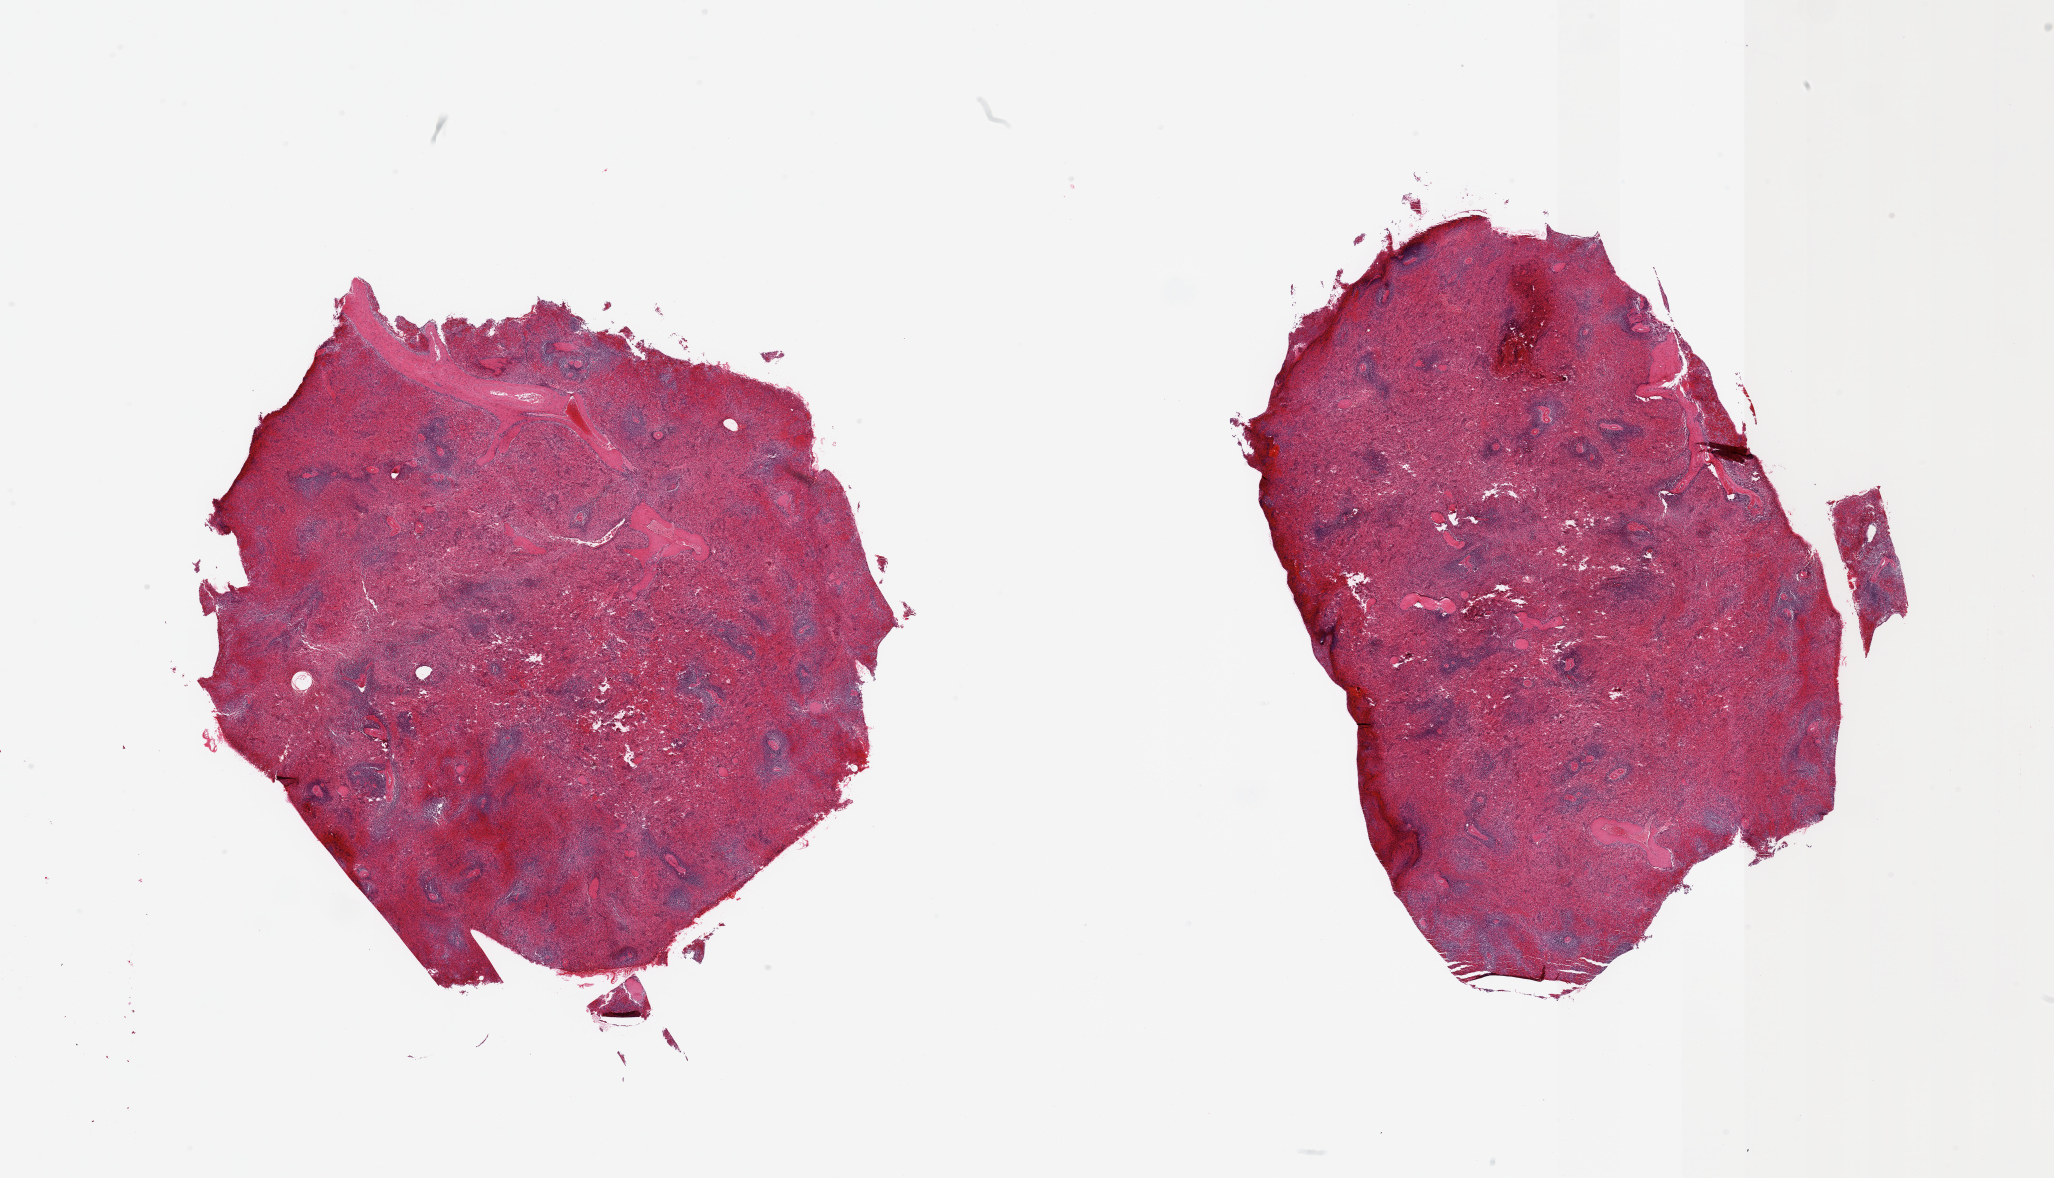
Whole-slide image, H&E stain, shown as a low-resolution overview of the whole scanned area (about 32.5 x 18.6 mm); PAXgene-fixed, paraffin-embedded tissue; sampled site (target tissue): spleen; tissue donor sample.
- reviewer comment on this tissue sample: 2 pieces; focally congested